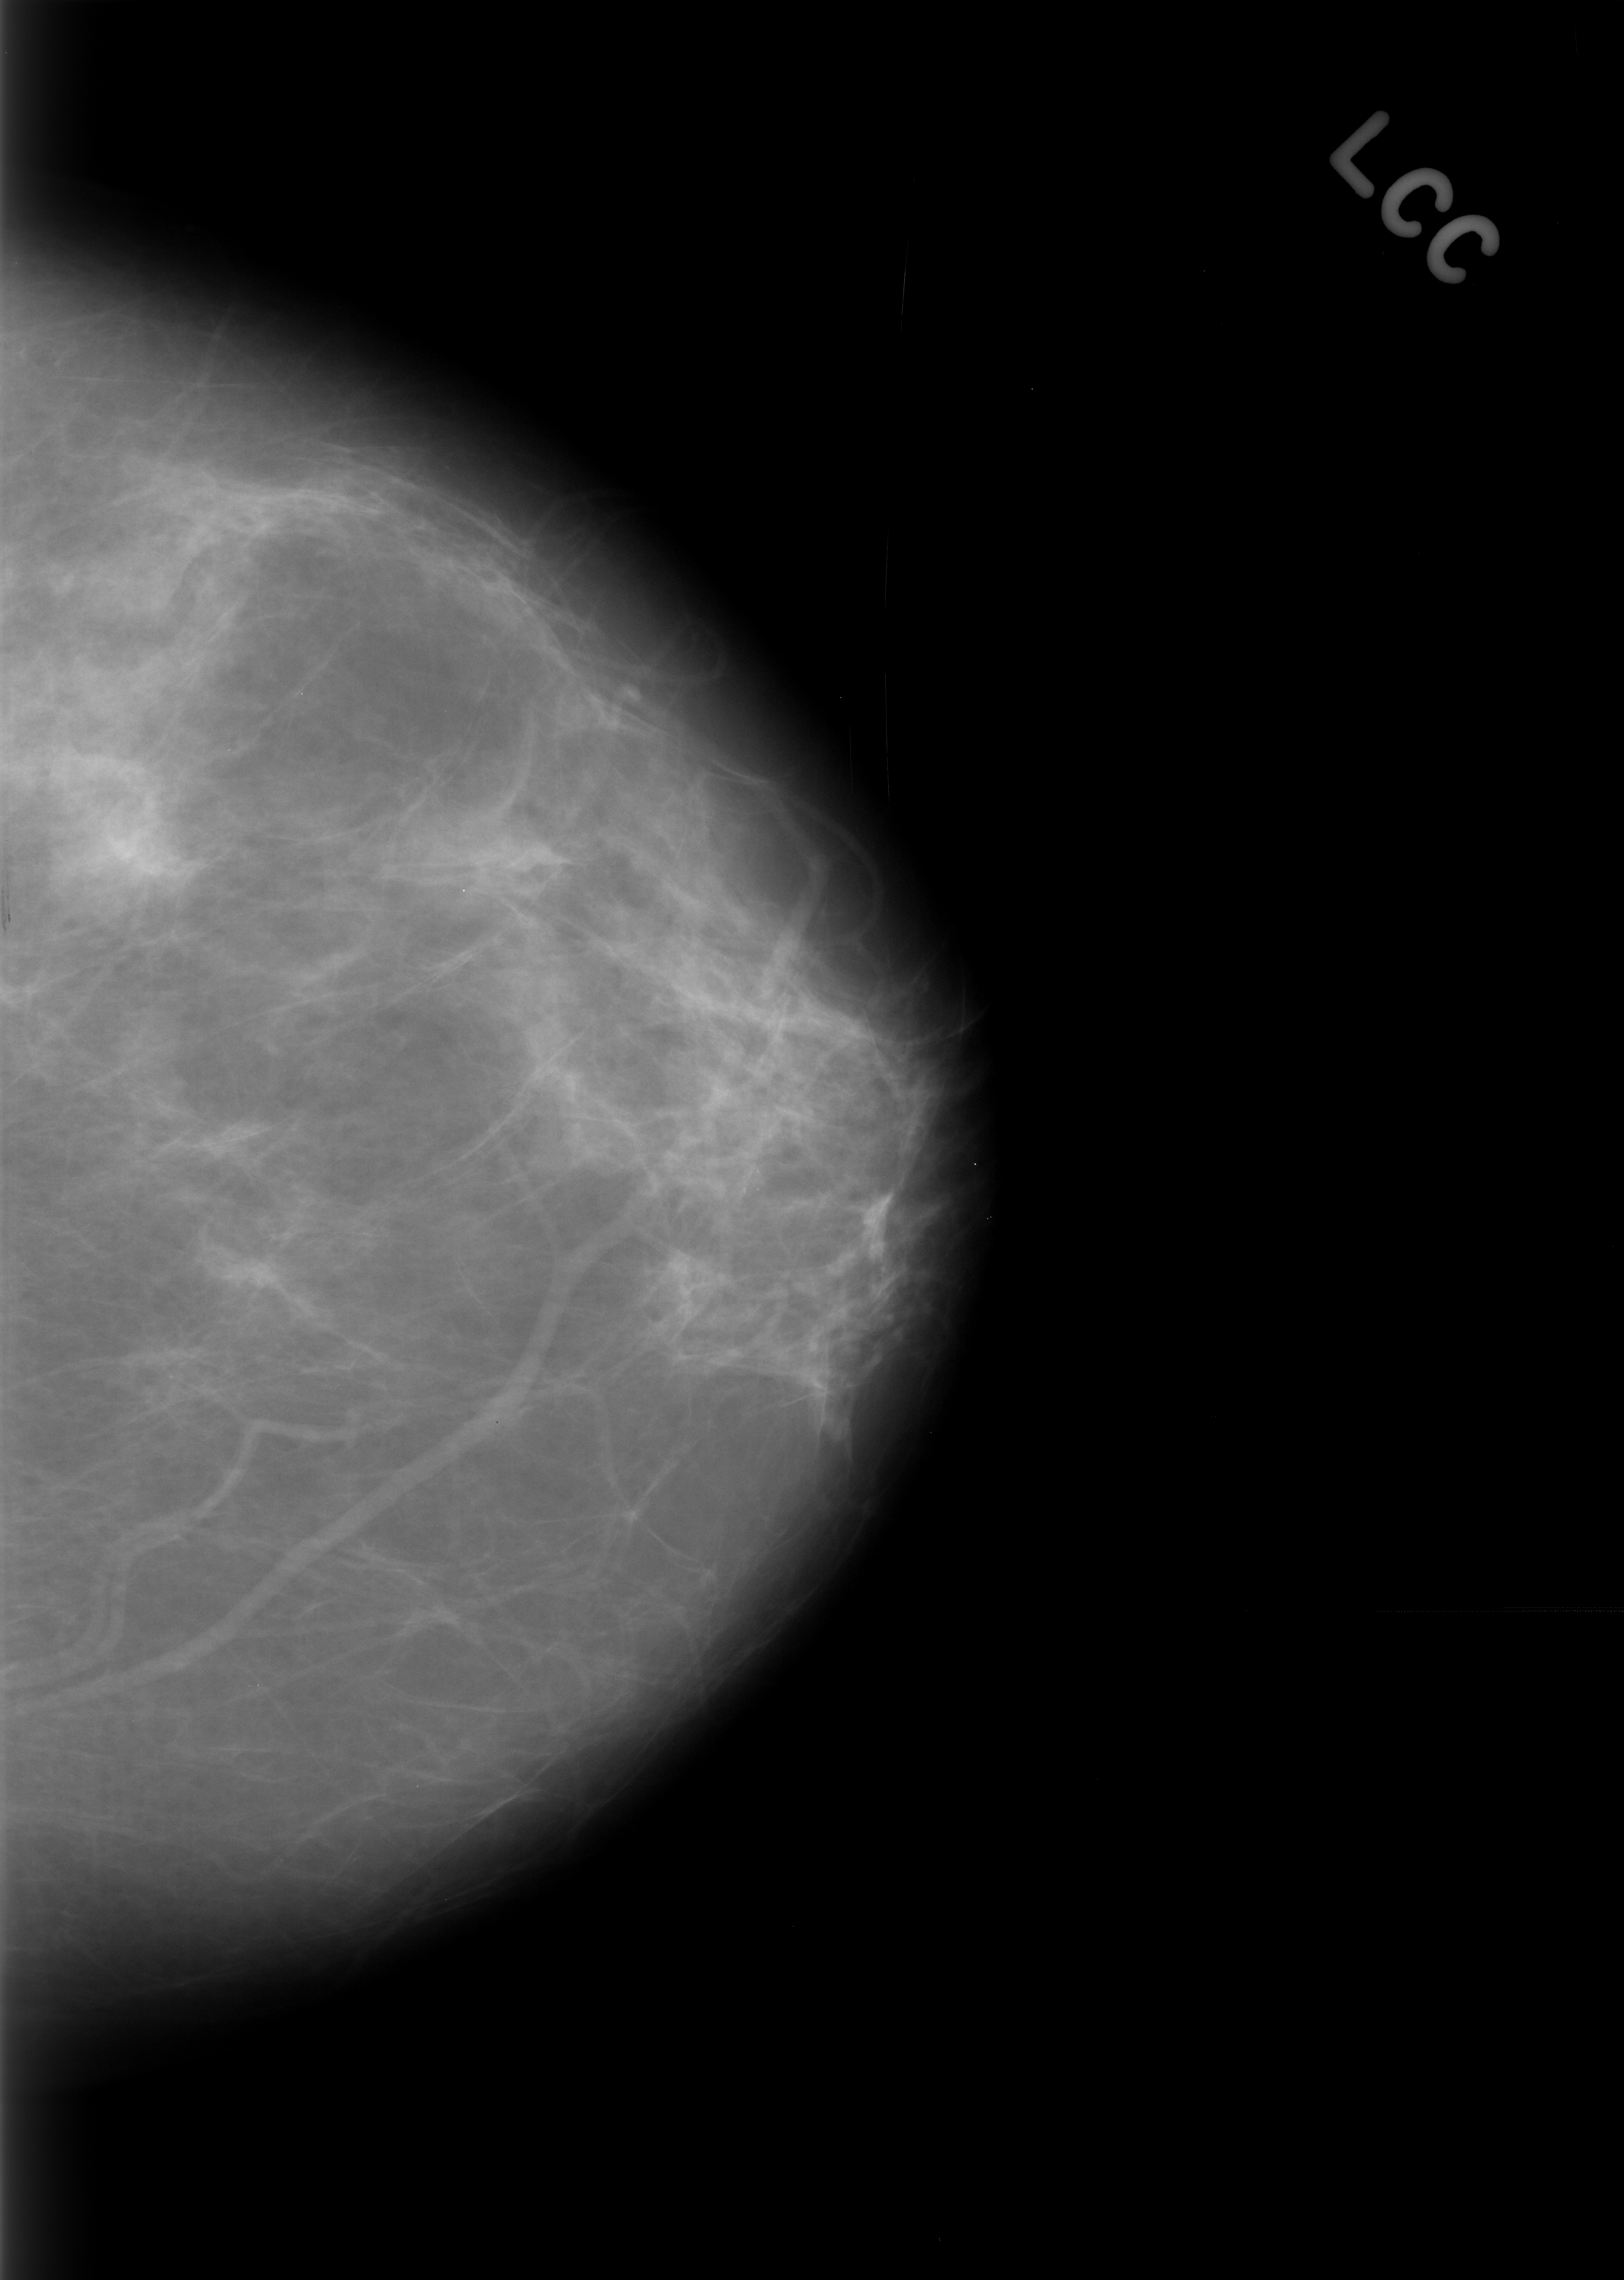
Scanned film-screen mammogram. Left breast. Craniocaudal (CC) view. Breast composition: almost entirely fatty (BI-RADS density category 1 of 4). 1624 × 2280 image matrix.
Expert-marked regions of interest on this film, with their recorded descriptors:
- mass, shape focal asymmetric density; BI-RADS assessment category 3; benign; no additional work-up was recommended (outcome (as recorded, no biopsy): benign without callback): bounding box (x1, y1, x2, y2) in pixels: (47, 785, 199, 927)